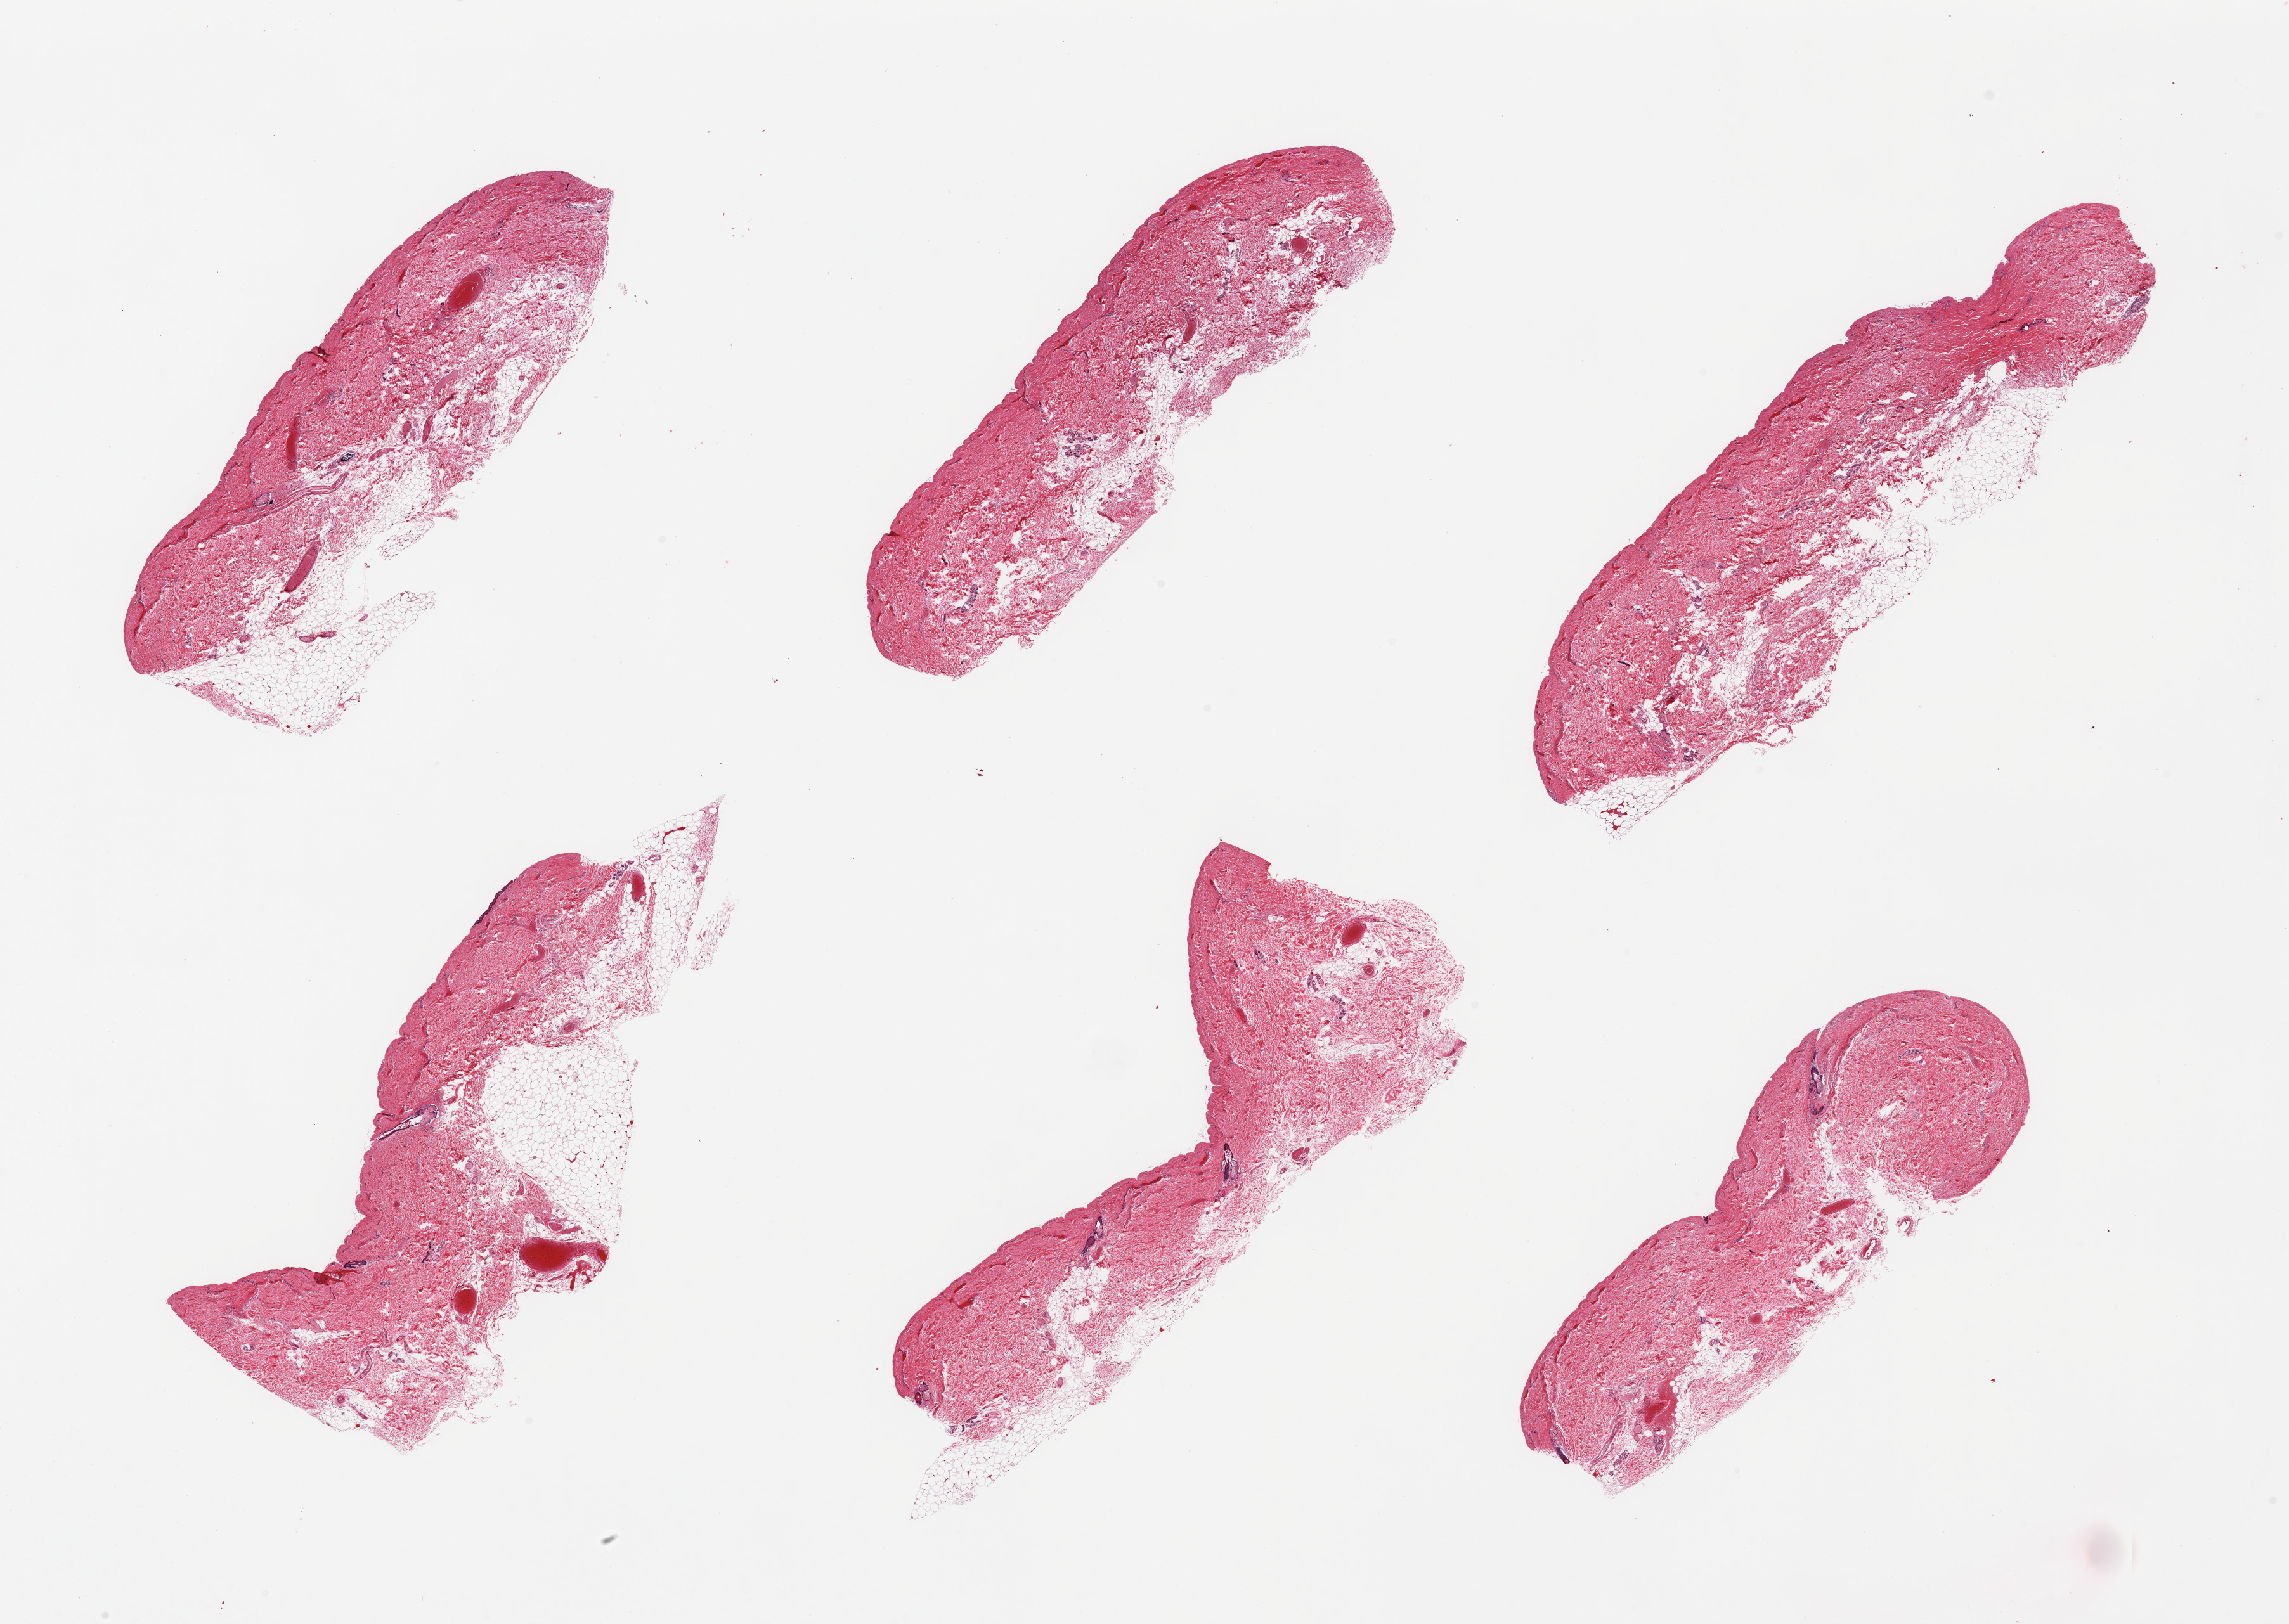
Haematoxylin and eosin whole-slide image, low-resolution overview of the scanned area, about 28.5 x 20.3 mm (slide scanned at 20x), PAXgene-fixed, paraffin-embedded tissue, target tissue: skin of lower leg, donor tissue sample. Donor sex: female.
Reviewer comment on this tissue sample: 6 pieces; up to 30% attached fat, only focal strip of epidermis measuring 49 microns.